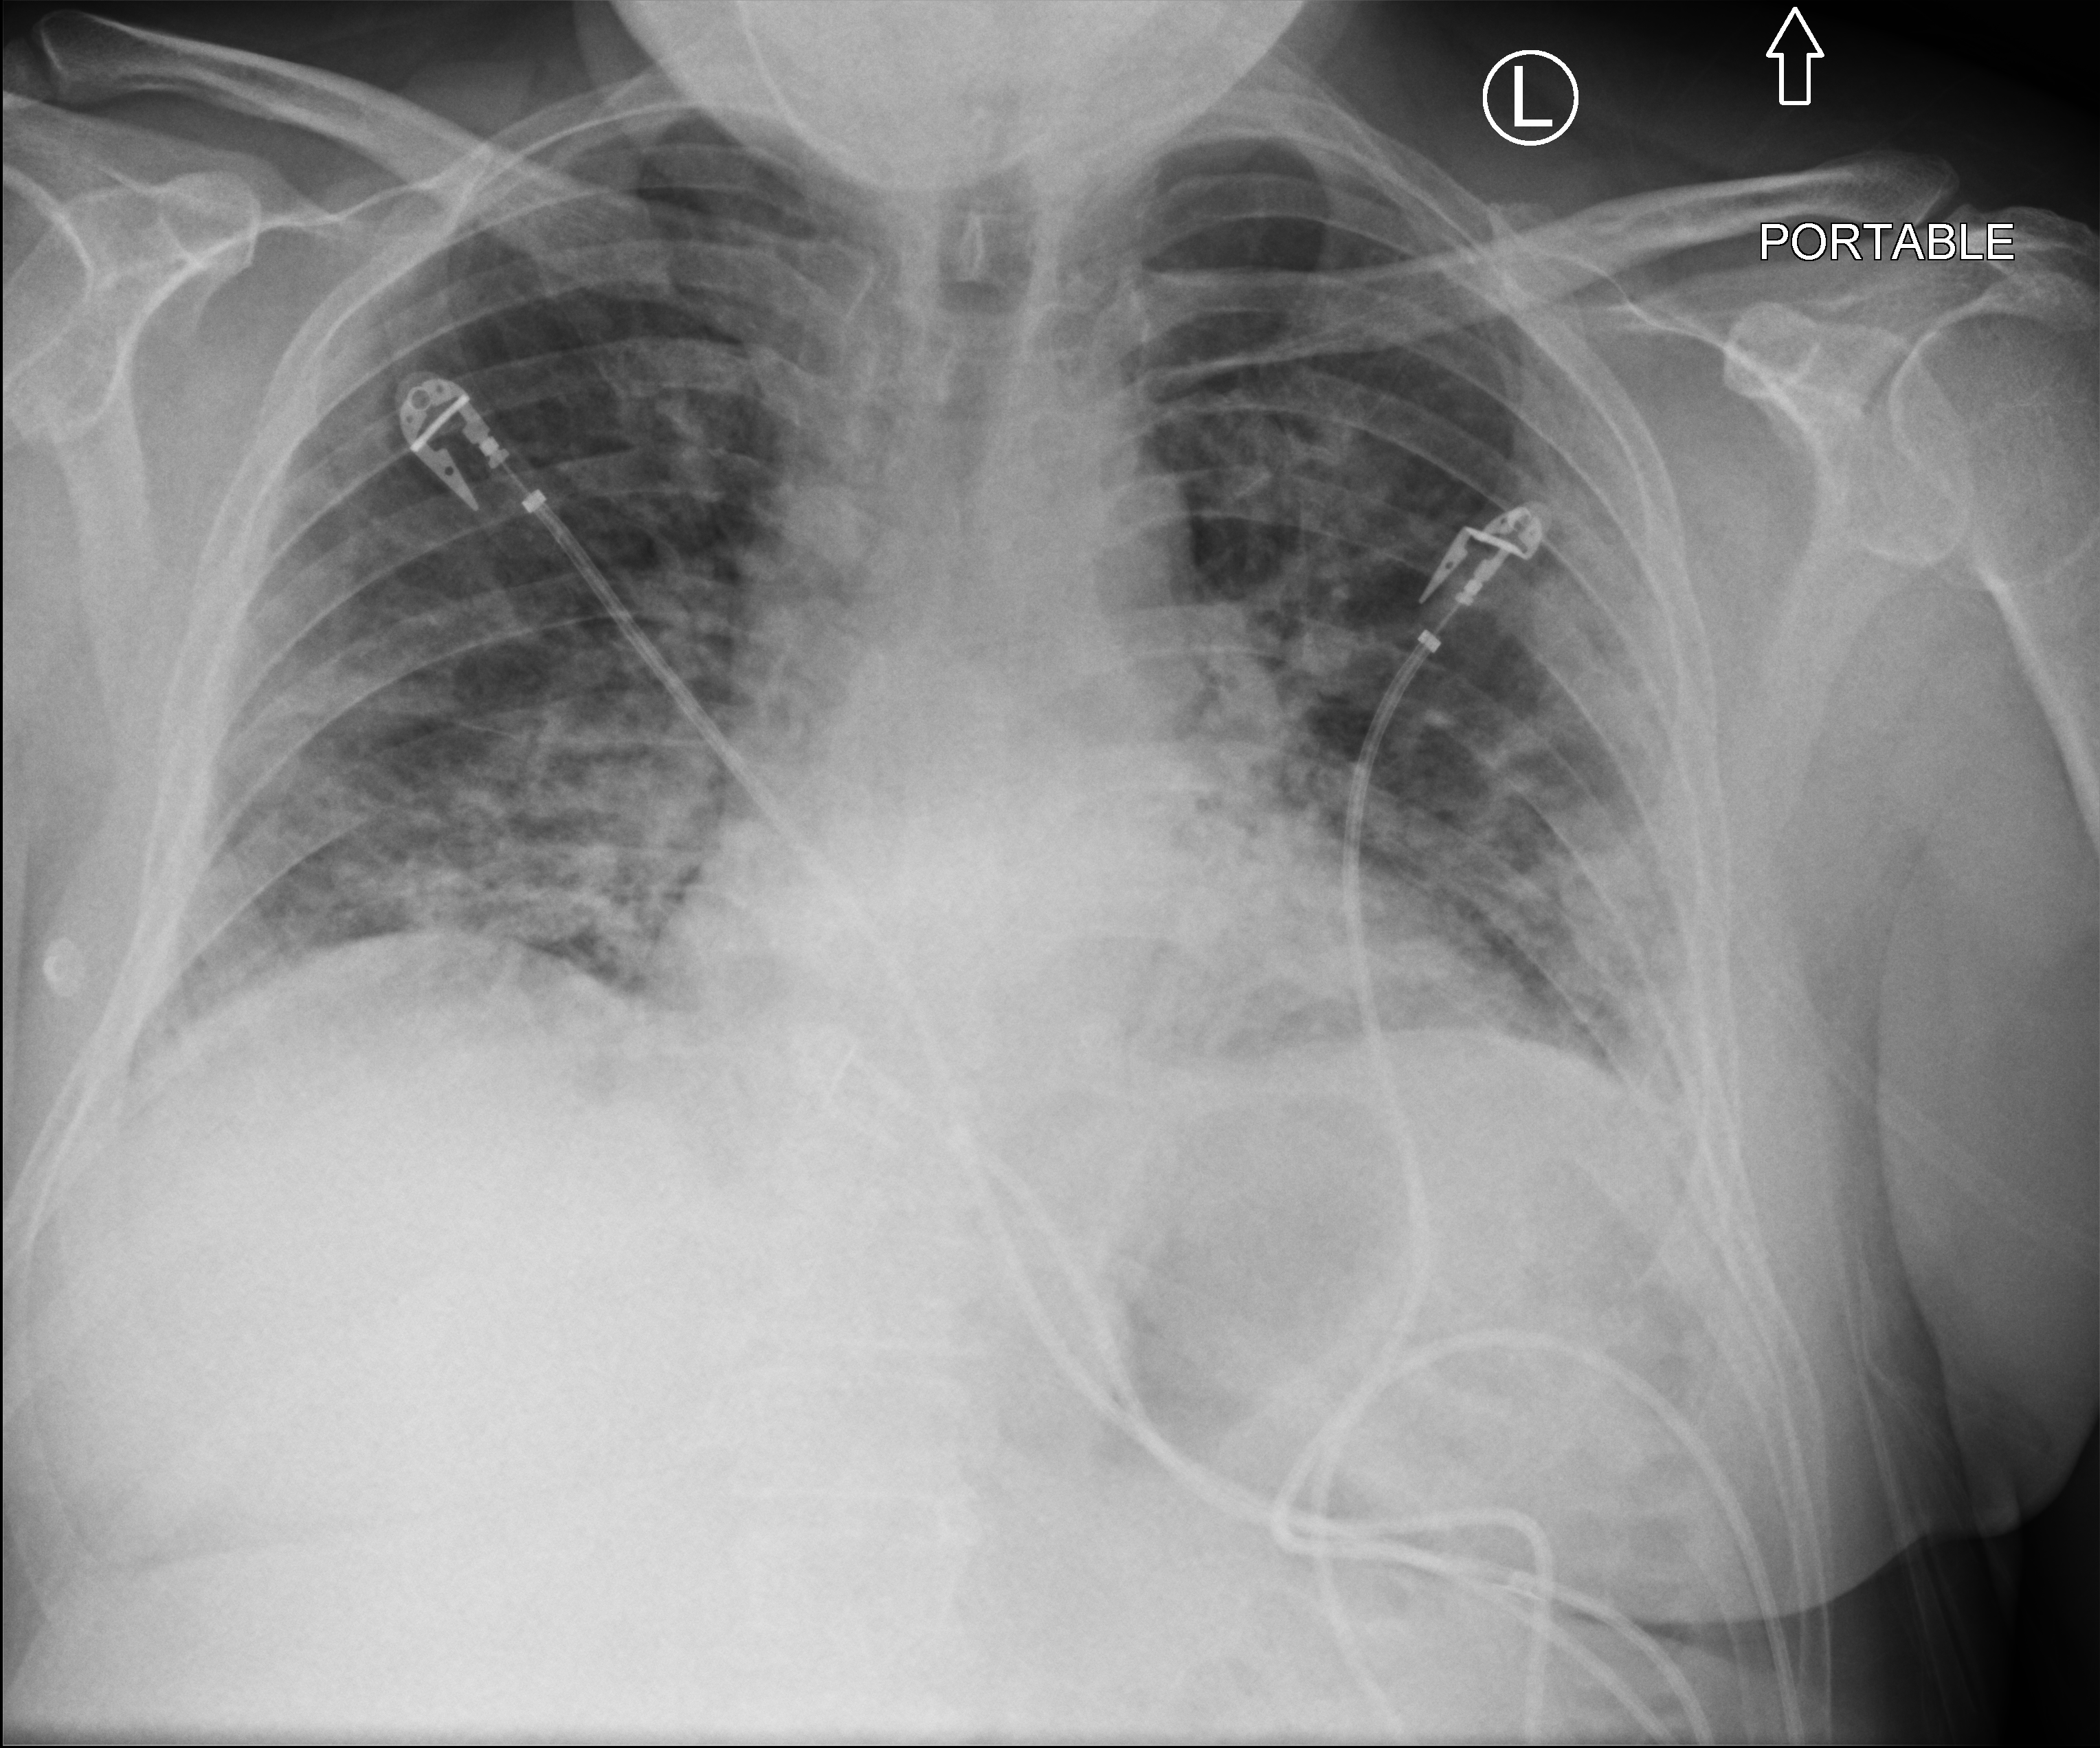
Chest X-ray (portable), anteroposterior (AP) projection. Patient hospitalised with COVID-19; male, aged 18–59 years.
From the hospital-stay record, not from the radiograph (when in the stay this image was taken is not recorded): smoking status (admission record): former.